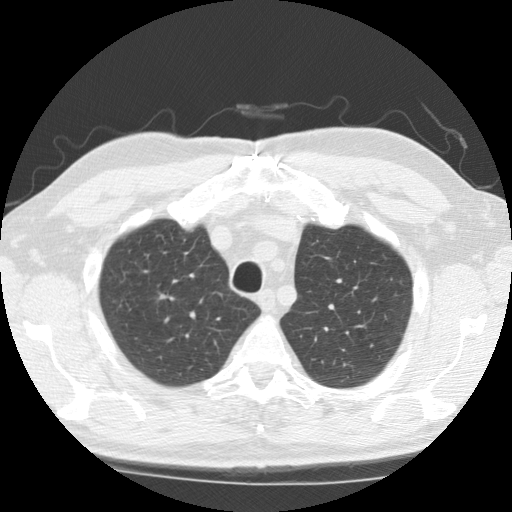
Low-dose screening chest CT, one axial slice; lung window (W 1500 / L -600 HU); 512 × 512 image matrix, field of view 350 × 350 mm.
Outlined on this slice (outlined manually by an expert reader):
- lesion 1 (tumor, upper lobe of right lung): bounding box <153,343,171,354> (left, top, right, bottom; pixels)